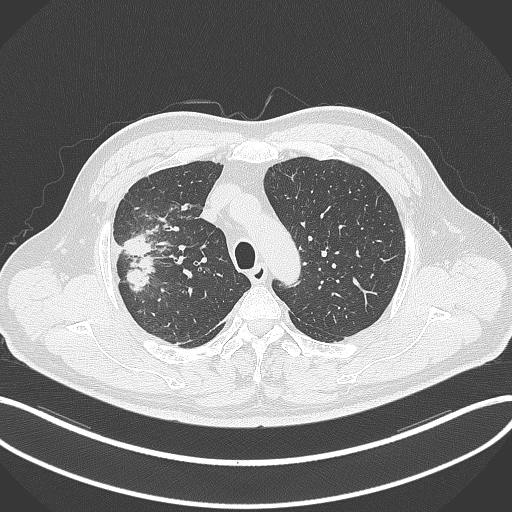
Chest CT, one axial slice; position 262 of 348 along the scan axis; lung window (W 1500 / L -600 HU); 512 × 512 image matrix. Male patient, age 55 years. From the clinical record (not read from this slice): clinical TNM (as recorded): T3 N2 M1.
Structures marked on this image (bounding box drawn by a radiologist):
- lung tumour (recorded histology: adenocarcinoma): bounding box <118,229,160,294> (left, top, right, bottom; pixels)